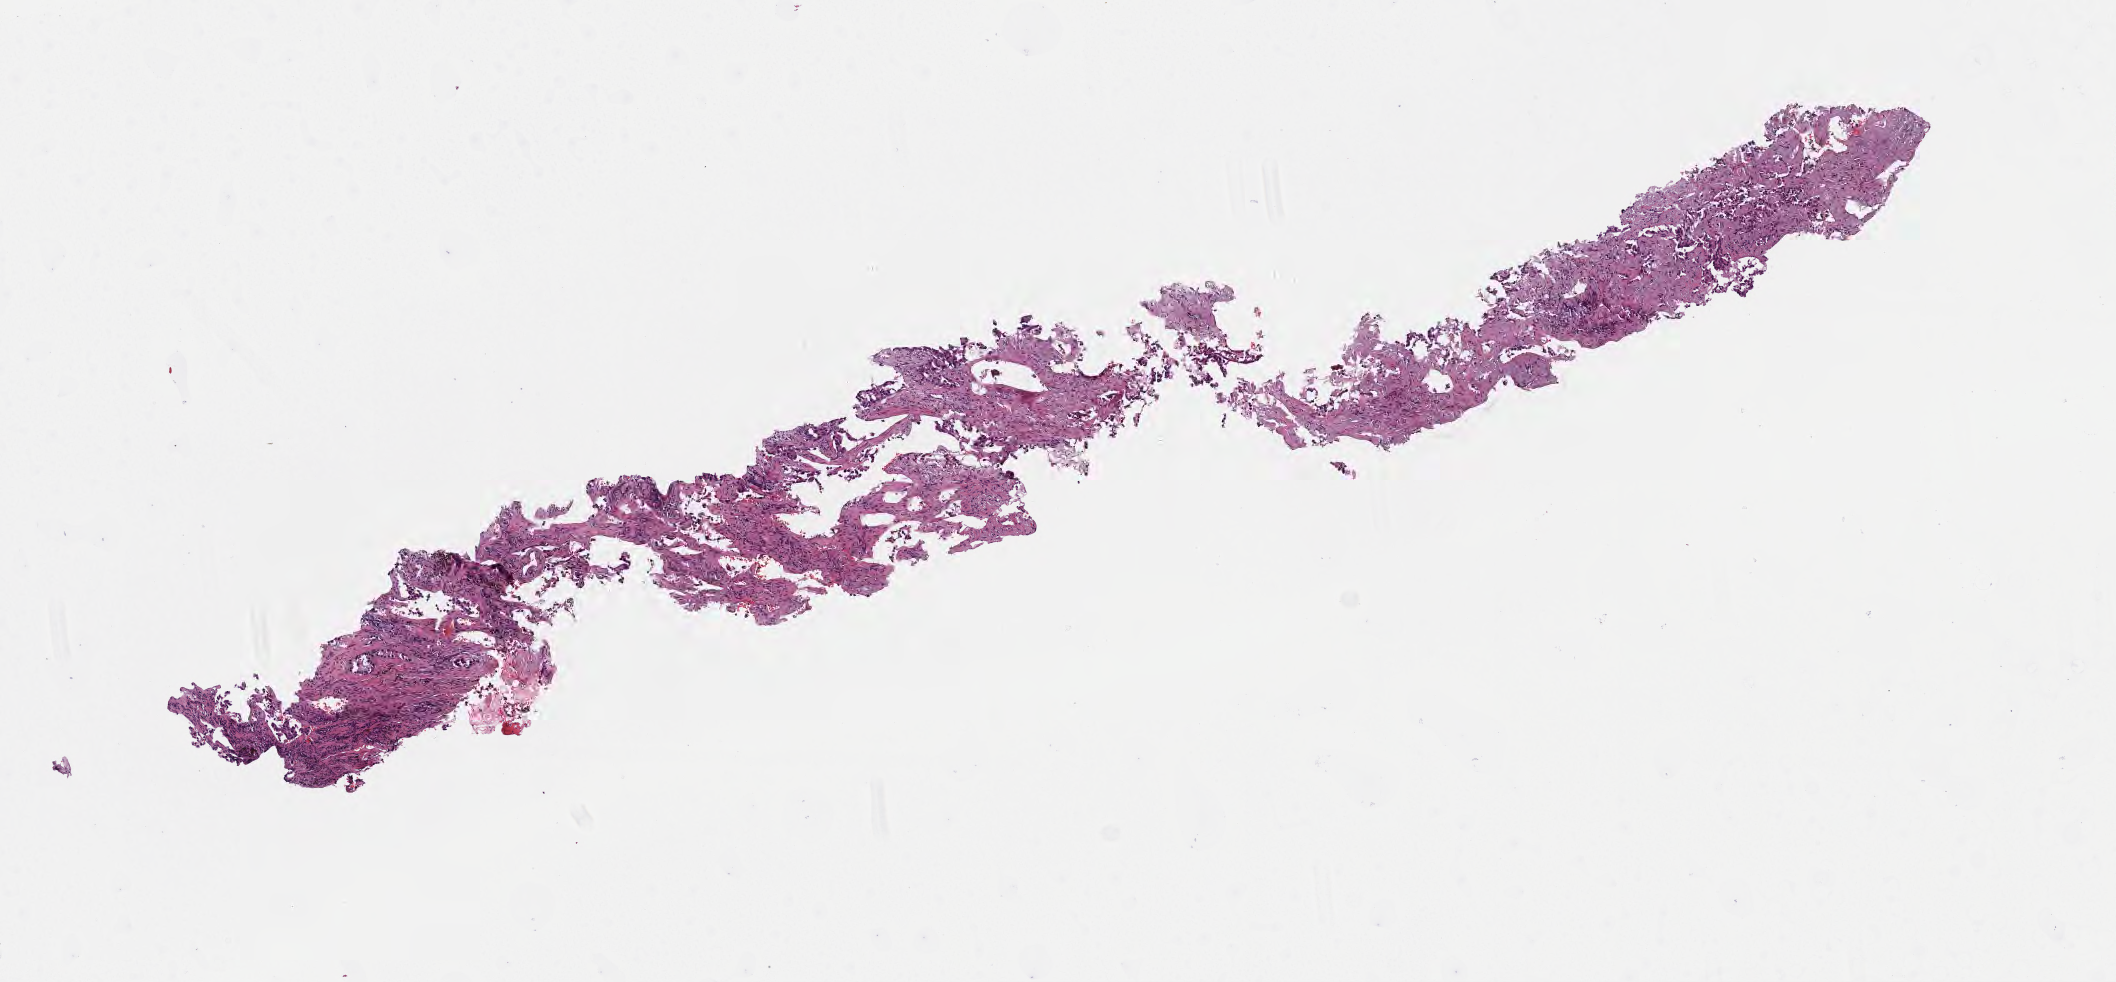
H&E whole-slide image — shown as a low-resolution overview of the whole scanned area (about 8.6 x 4.0 mm), specimen: tumor tissue, site: lung. Patient male; aged 67.
Histologic diagnosis: Adenocarcinoma, NOS.